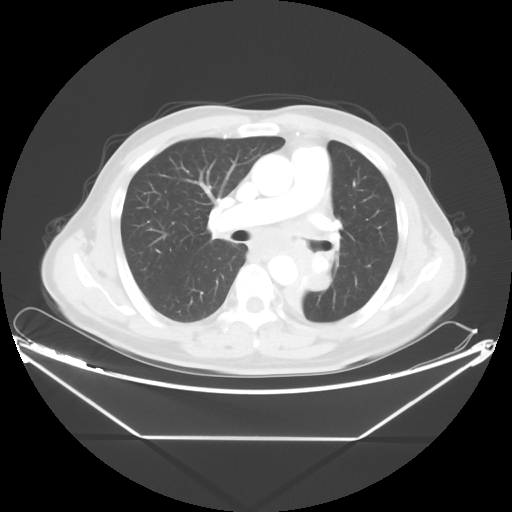
Chest CT, one axial slice; position 27 of 48 along the scan axis; reconstruction kernel STANDARD; 120 kVp; lung window (W 1500 / L -600 HU); 5 mm slice thickness; 512 × 512 image matrix. Patient: male, 58 years. From the clinical record (not read from this slice): clinical TNM (as recorded): T3 N3 M0.
Structures marked on this image (bounding box drawn by a radiologist):
- lung tumour (recorded histology: squamous cell carcinoma): bounding box <280,235,333,318> (left, top, right, bottom; pixels)